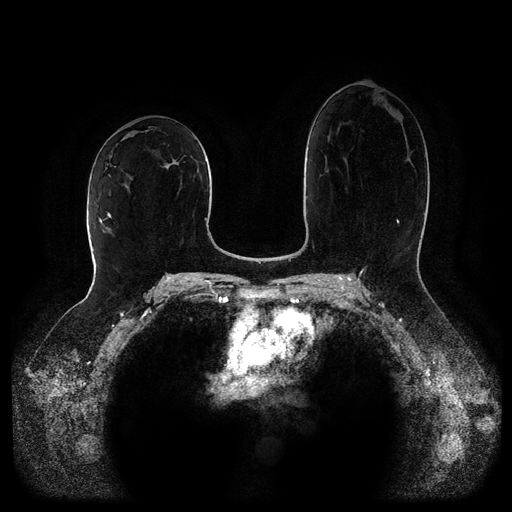
Breast MRI (dynamic contrast-enhanced, multi-phase), one axial slice. Position 53 of 116 along the scan axis. Dynamic contrast-enhanced series, time point 2 of 5 at this slice position (early post-contrast). 1.5 T. TE 2.6 ms, TR 5.2 ms. 2 mm slice thickness. 512 × 512 image matrix. Patient: female, 52 years.
Outlined on this slice (semi-automatically segmented with operator editing):
- breast lesion (labelled 'tumour' in the annotation; benign lesions carry a separate 'benign' label): bounding box [x1, y1, x2, y2] px = [164, 155, 185, 169]